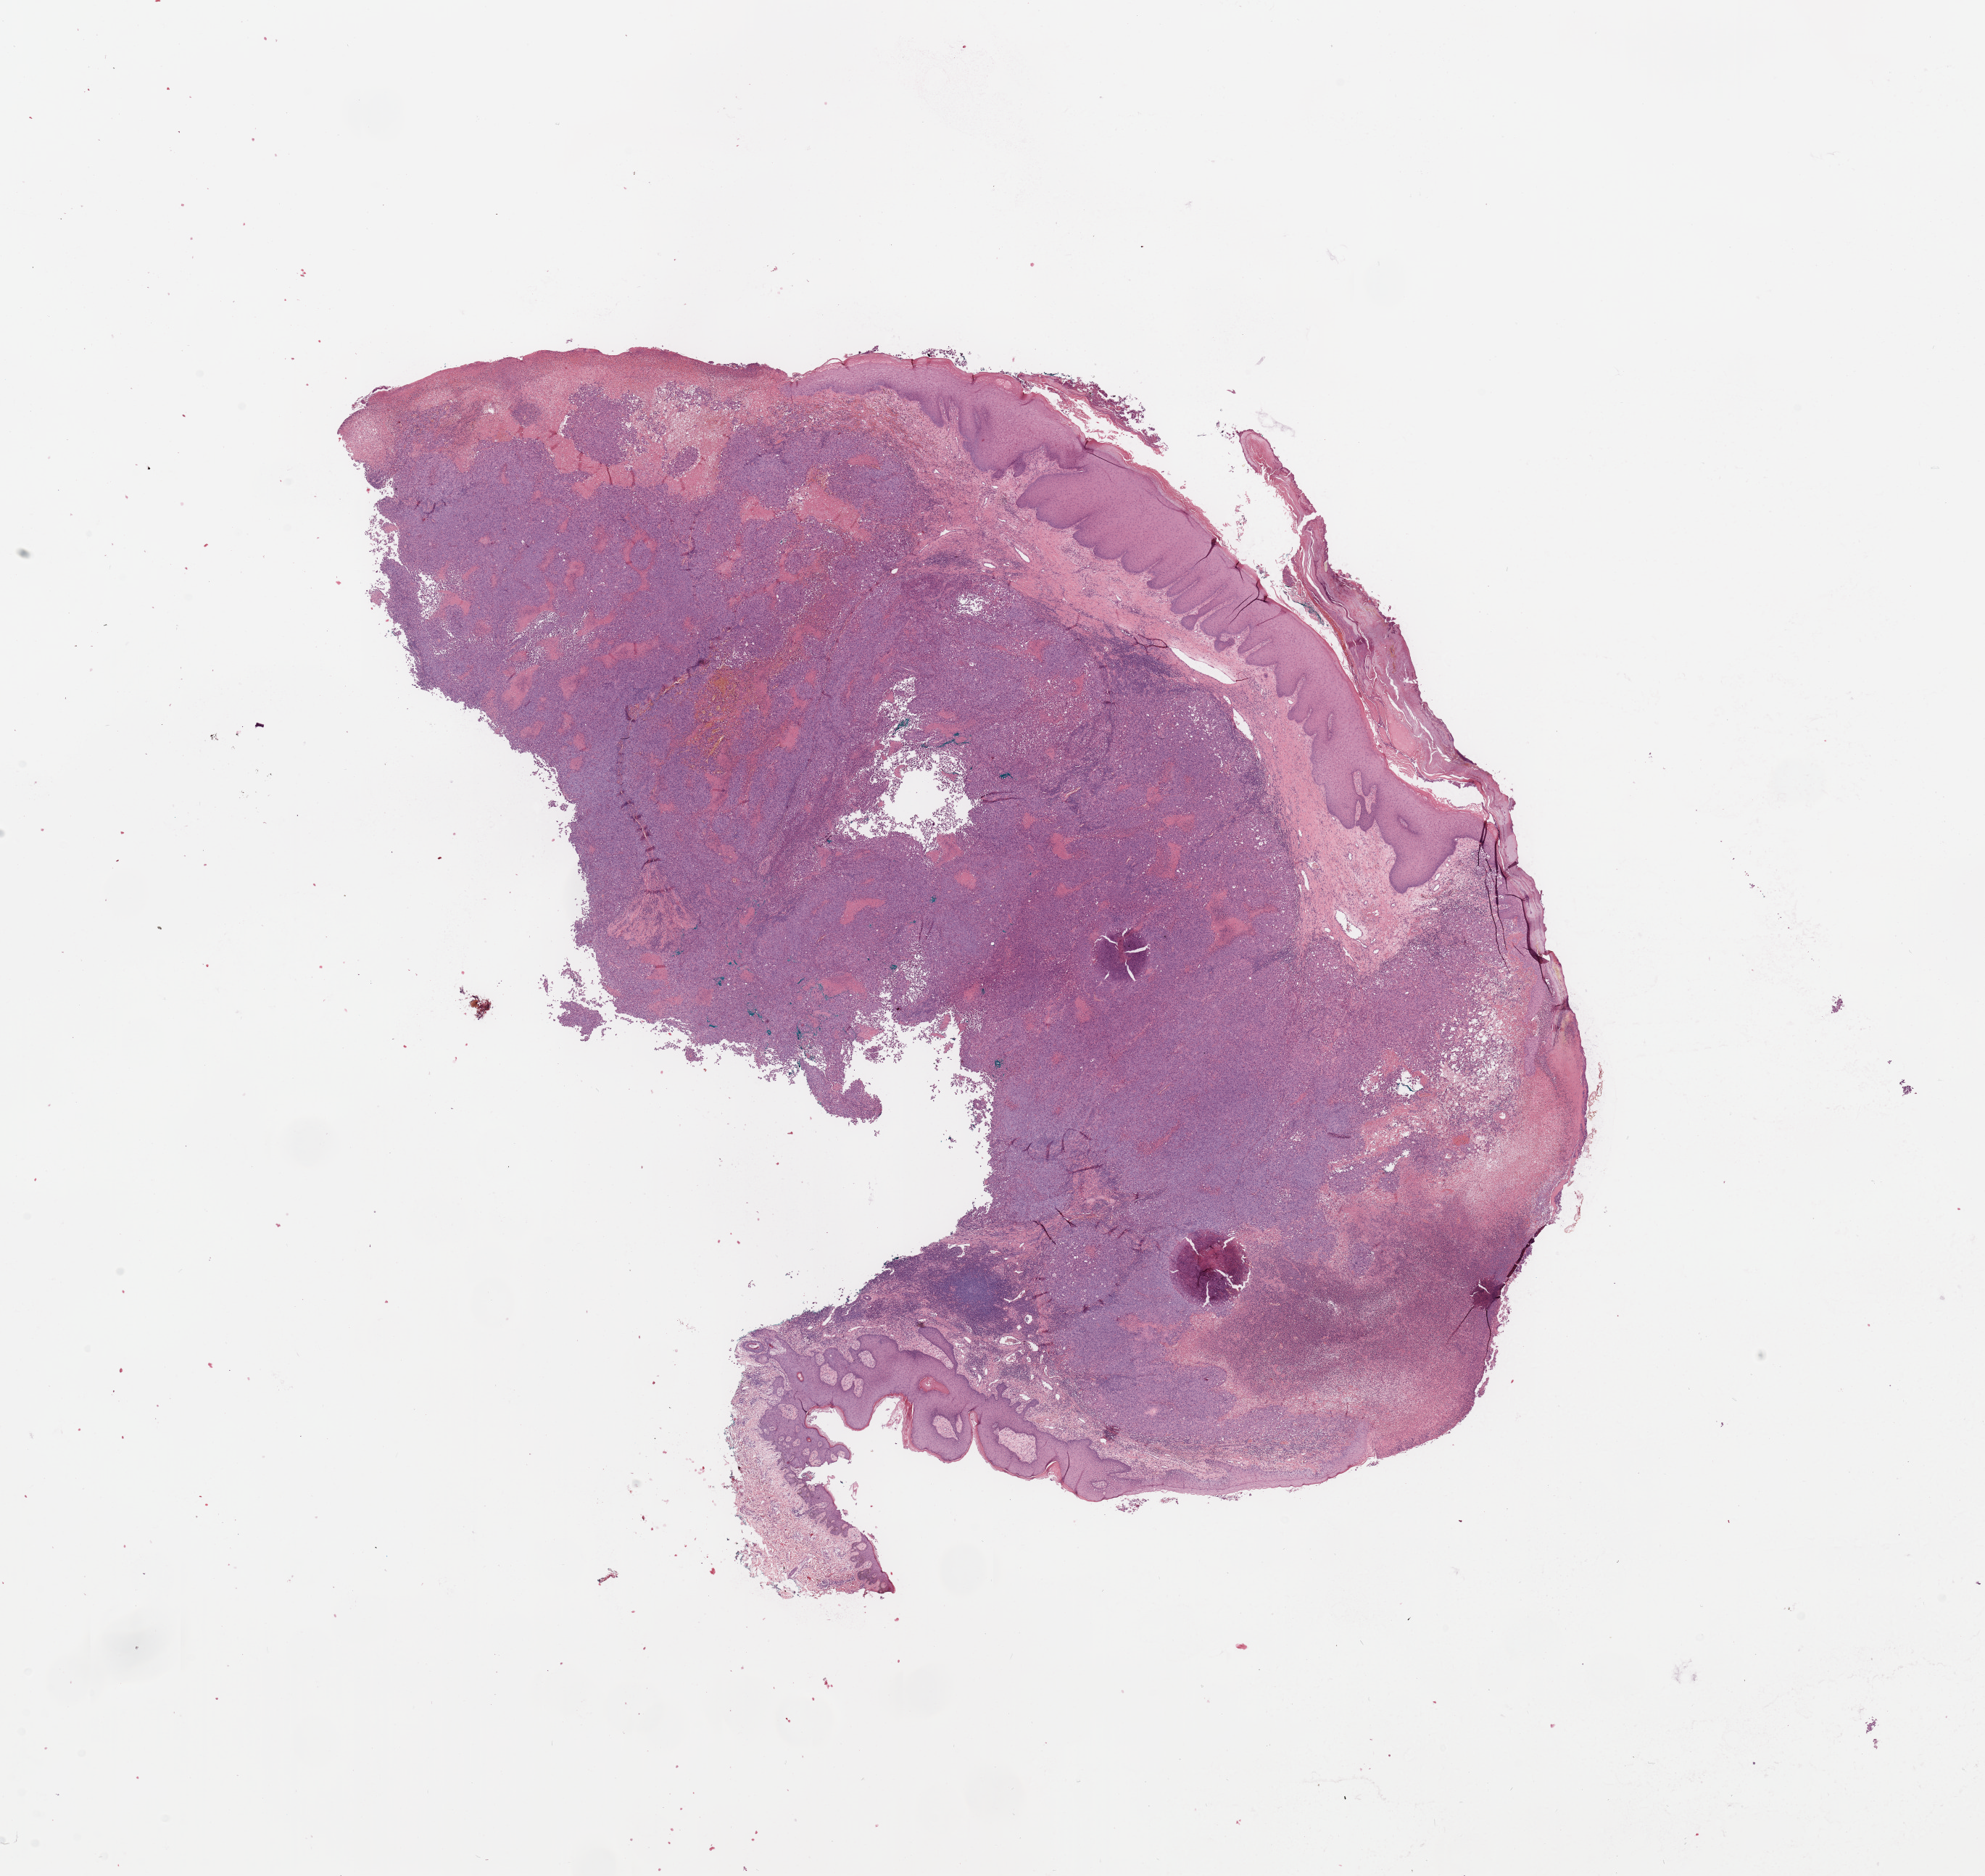
Digitized H&E-stained tissue section (whole slide) — low-resolution overview of the scanned area, about 21.7 x 20.5 mm (acquisition: 20x scan). Melanoma tumour tissue; sampled site not recorded. 57-year-old male patient.
AJCC pathologic stage: IIC. Primary tumour site (as recorded): trunk. Diagnosis: Malignant melanoma, NOS.